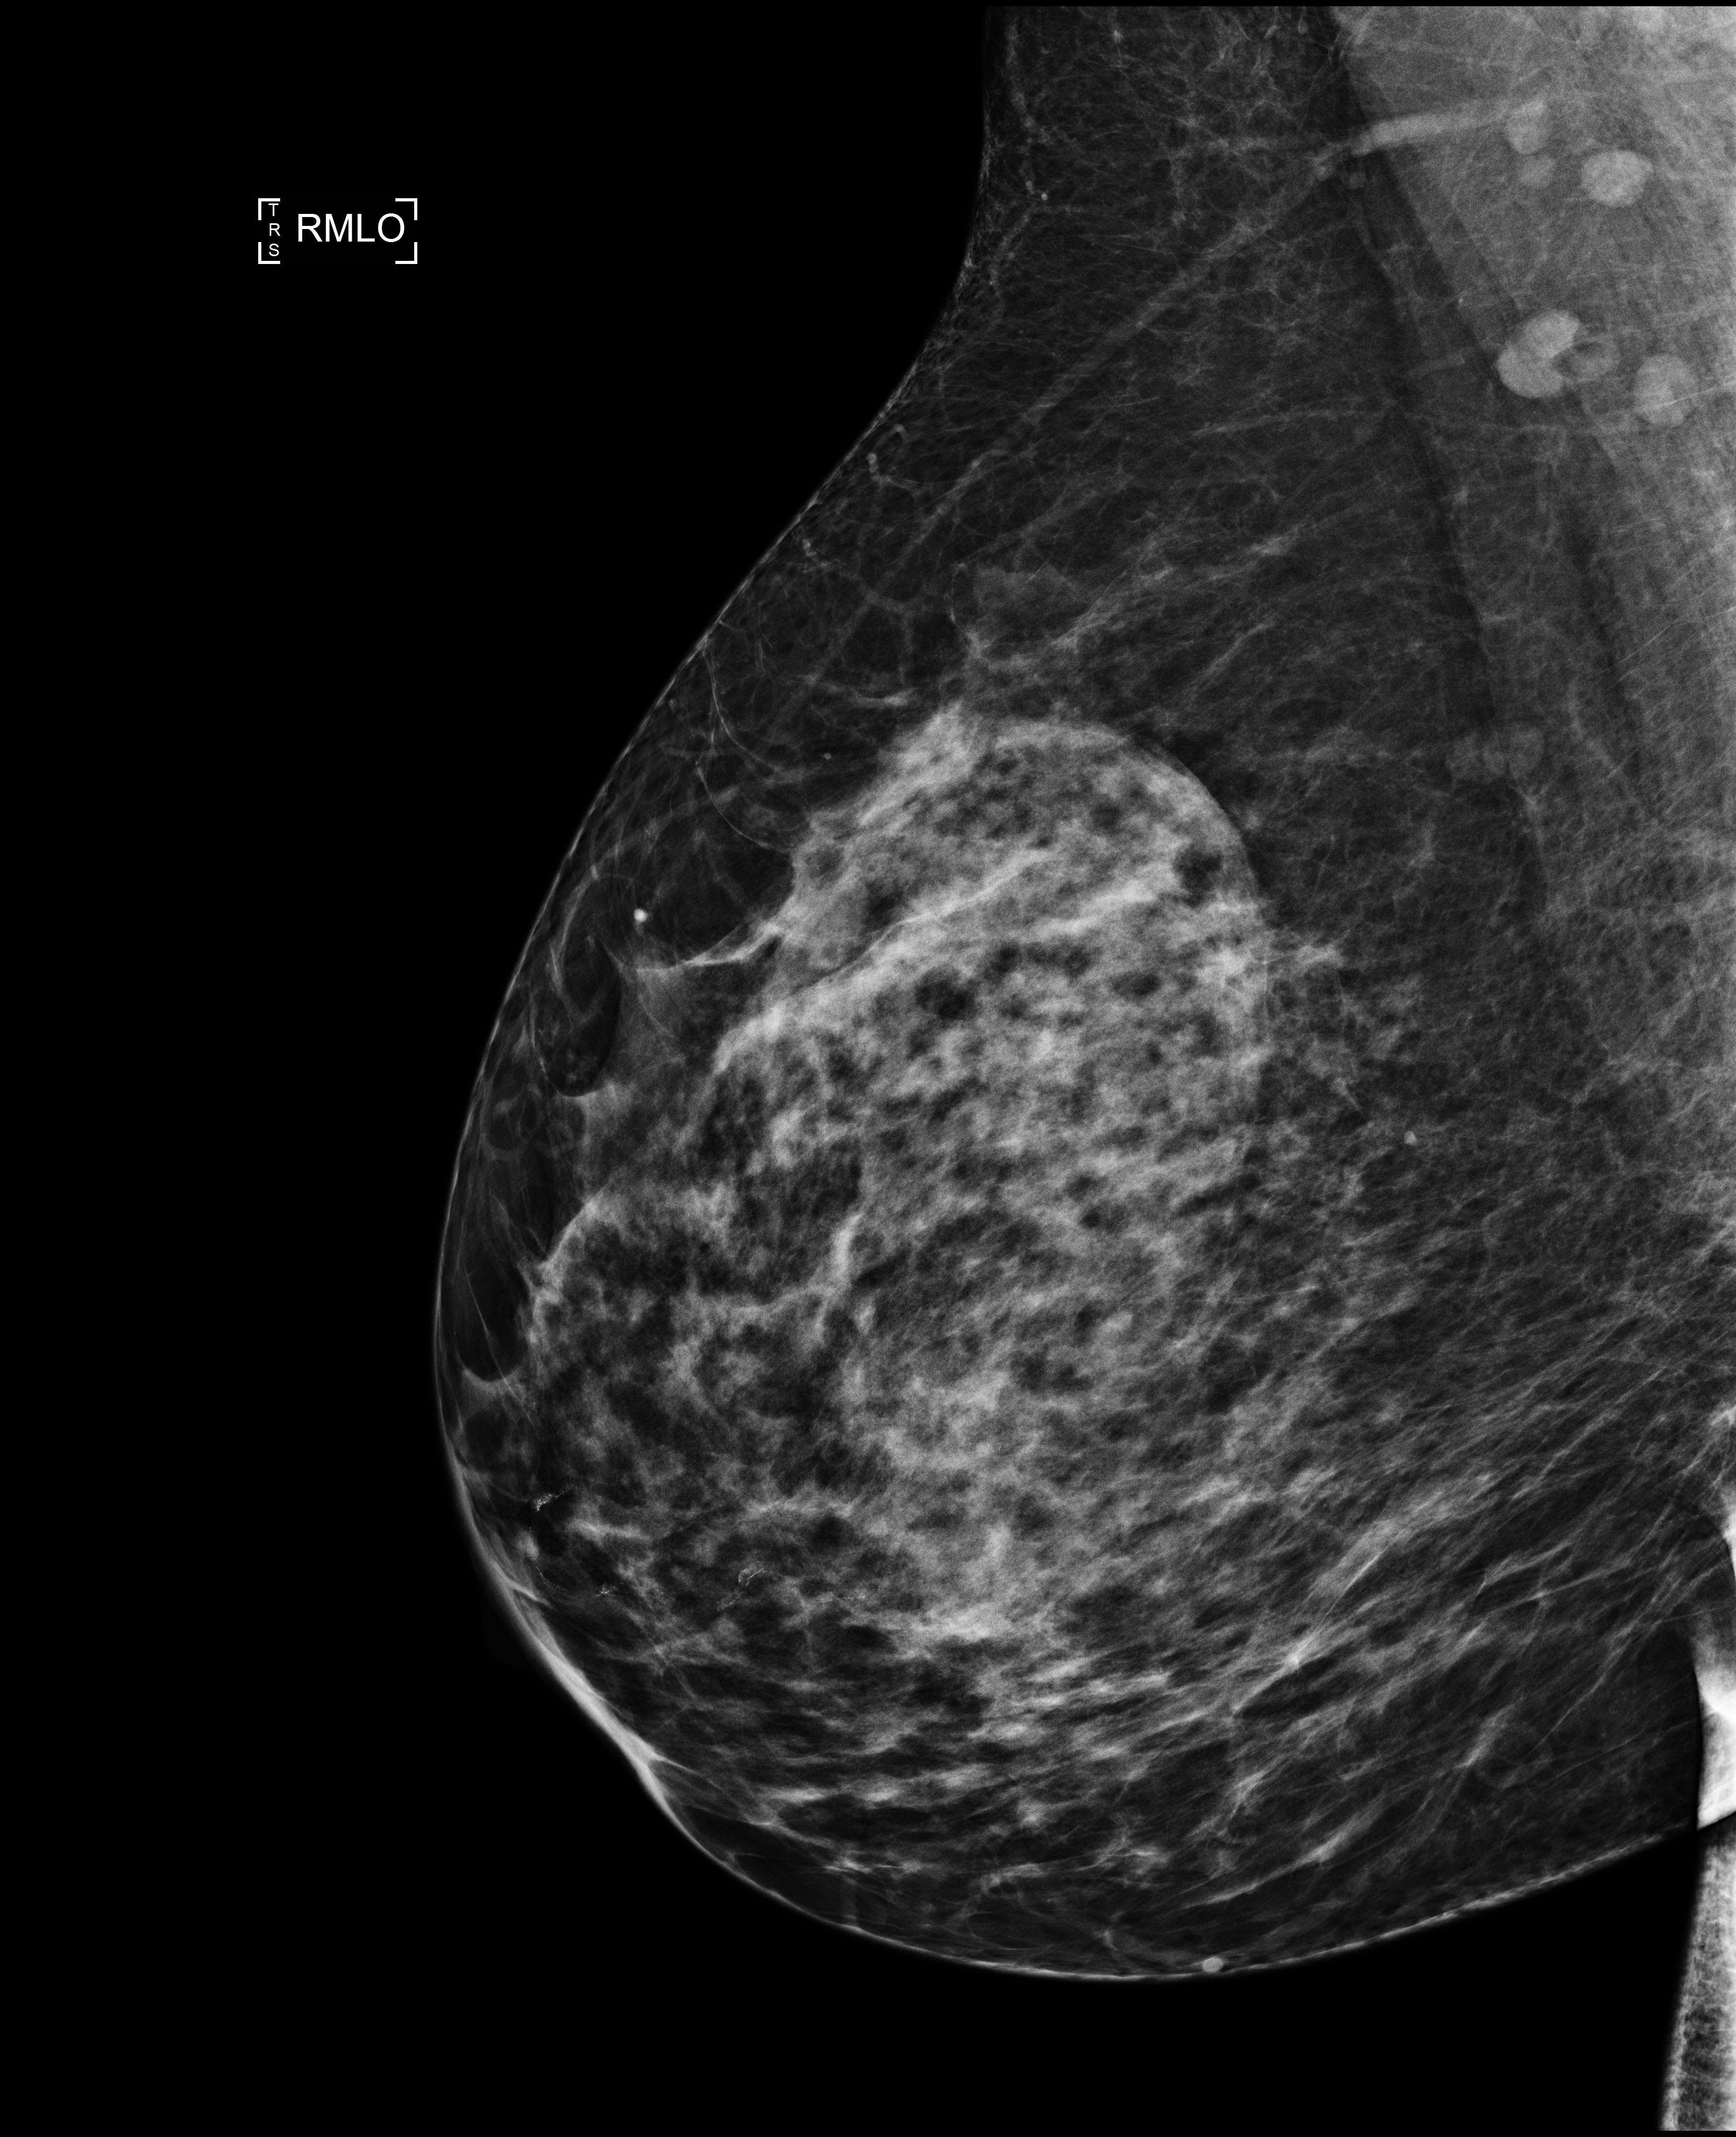
Annual screening mammography examination. Patient: female, 45 years.
Image type: full-field digital mammogram. Breast: right. Projection: MLO view.